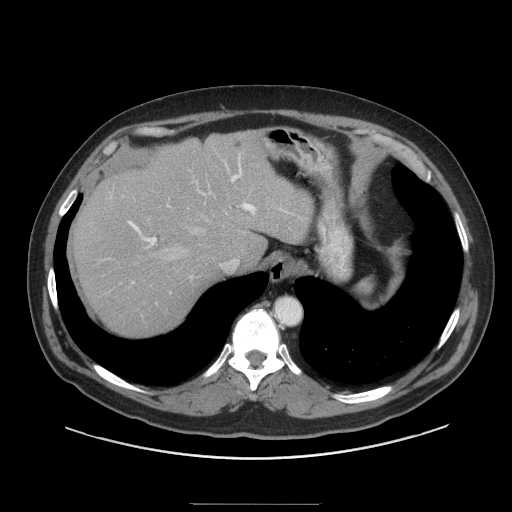
Contrast-enhanced abdominal CT (liver protocol), one axial slice. Slice 74 of 91 in the series (ordered by position). 140 kVp. Soft-tissue window (W 400 / L 40 HU). 2.5 mm slice thickness. 512 × 512 image matrix, field of view 440 × 440 mm. Case-level facts recorded for this patient, not image findings: diagnosis: hepatocellular carcinoma (patient treated with transarterial chemoembolisation; whether this scan precedes or follows treatment is not stated here); TNM stage (as recorded): Stage-I; Child-Pugh class: A; tumour nodularity: uninodular; tumour size: 4 cm.
Outlined on this slice (semi-automatically segmented with operator editing):
- abdominal aorta: bounding box [x1, y1, x2, y2] px = [276, 298, 300, 323]
- liver parenchyma outside the tumour (the mass and vessels are separate outlines, so this box may not span the whole liver): [72, 130, 314, 336]
- liver vessels: [128, 156, 282, 263]